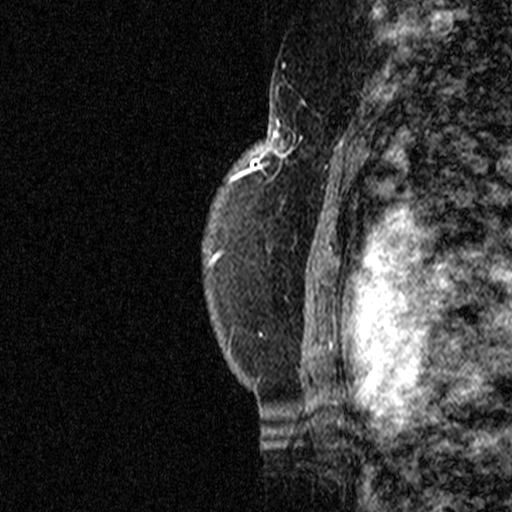
Breast MRI (dynamic contrast-enhanced), one sagittal slice; position 34 of 44 along the scan axis; dynamic contrast-enhanced study with each time point stored as its own series, time point 2 of 3 at this slice position (early post-contrast, ordered by acquisition time); 1.5 T; TE 4.5 ms, TR 11 ms; 3 mm slice thickness; 512 × 512 image matrix, field of view 200 × 200 mm. Patient: female, 49 years. From the clinical record (not read from this slice): setting: breast cancer imaged before/during neoadjuvant chemotherapy; receptor status: triple-negative.
Annotated regions visible in this slice (semi-automatic segmentation, software-assisted and operator-edited):
- analysis volume of interest (the breast-tissue region the enhancement analysis was run in; not a lesion): bounding box [x1, y1, x2, y2] px = [254, 112, 347, 207]
- tumour enhancement mask (voxels above the 90 % enhancement threshold inside the analysis volume of interest): [254, 120, 341, 207]